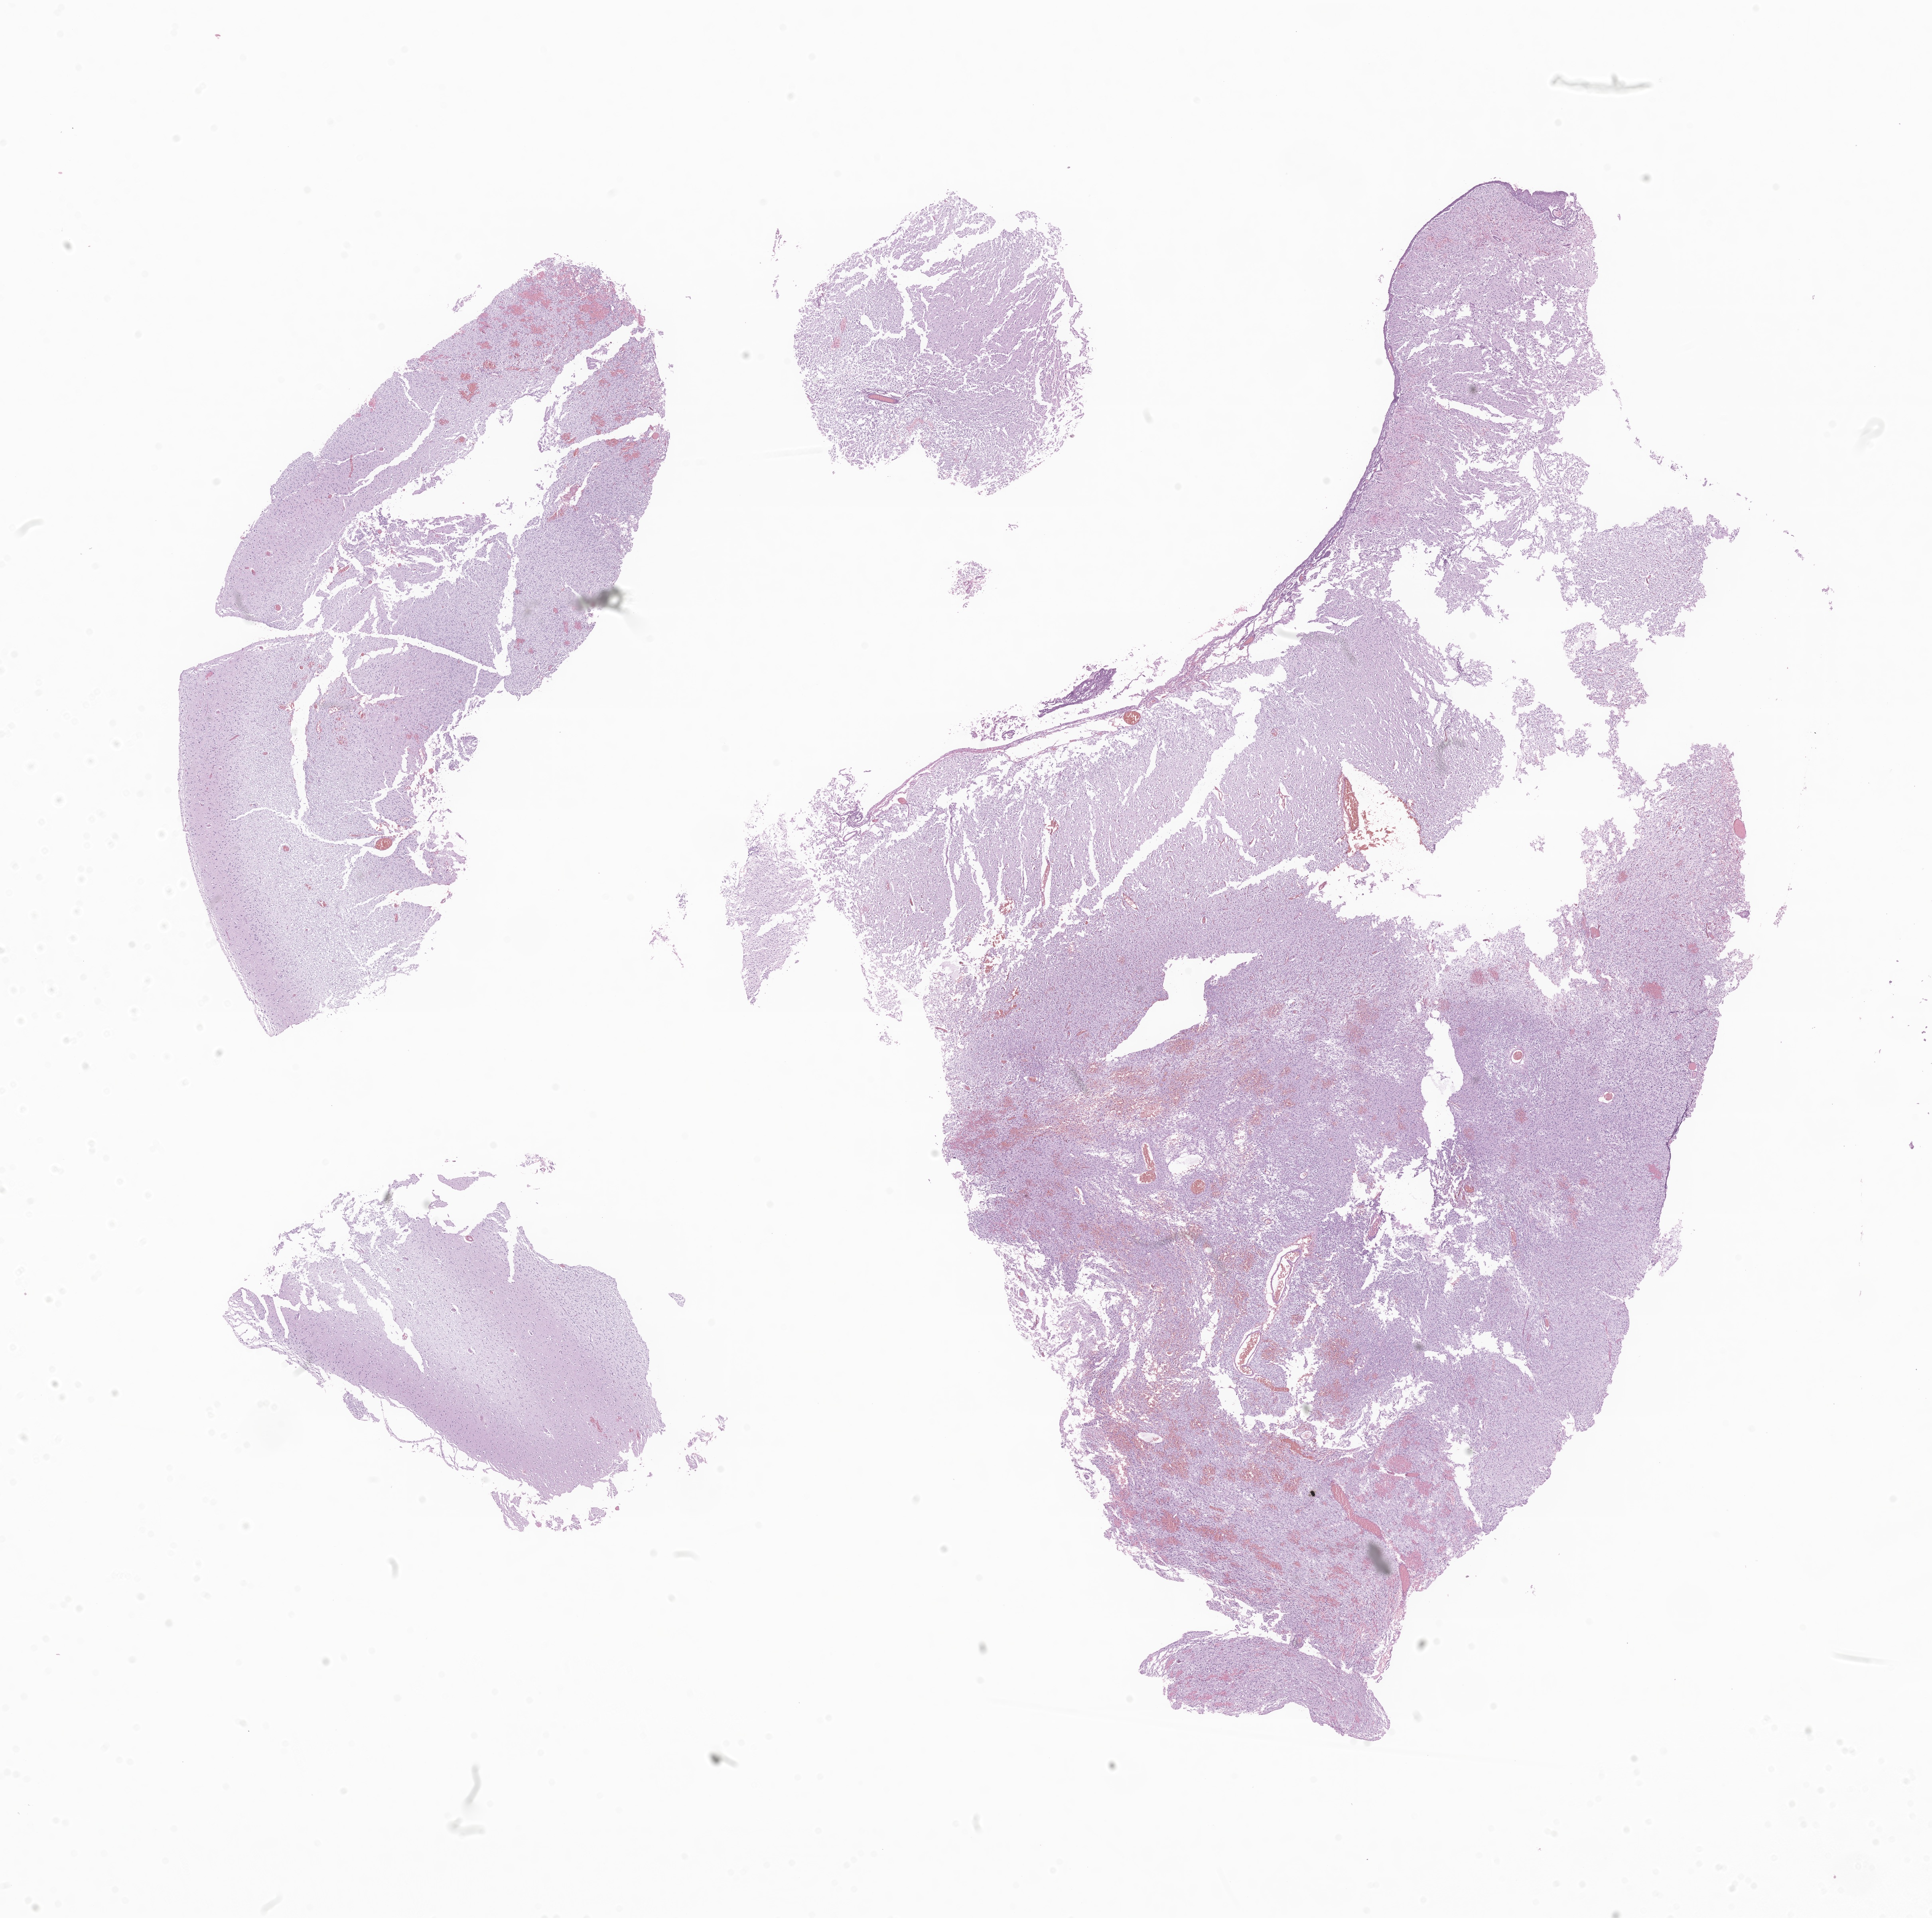
Digitized haematoxylin and eosin-stained section of tumor tissue from the brain — whole scanned area (about 20.4 x 20.3 mm) shown as a low-resolution overview; FFPE section. Patient: male, age 944 days (about 2.6 years).
- recorded diagnosis: Glioma, malignant